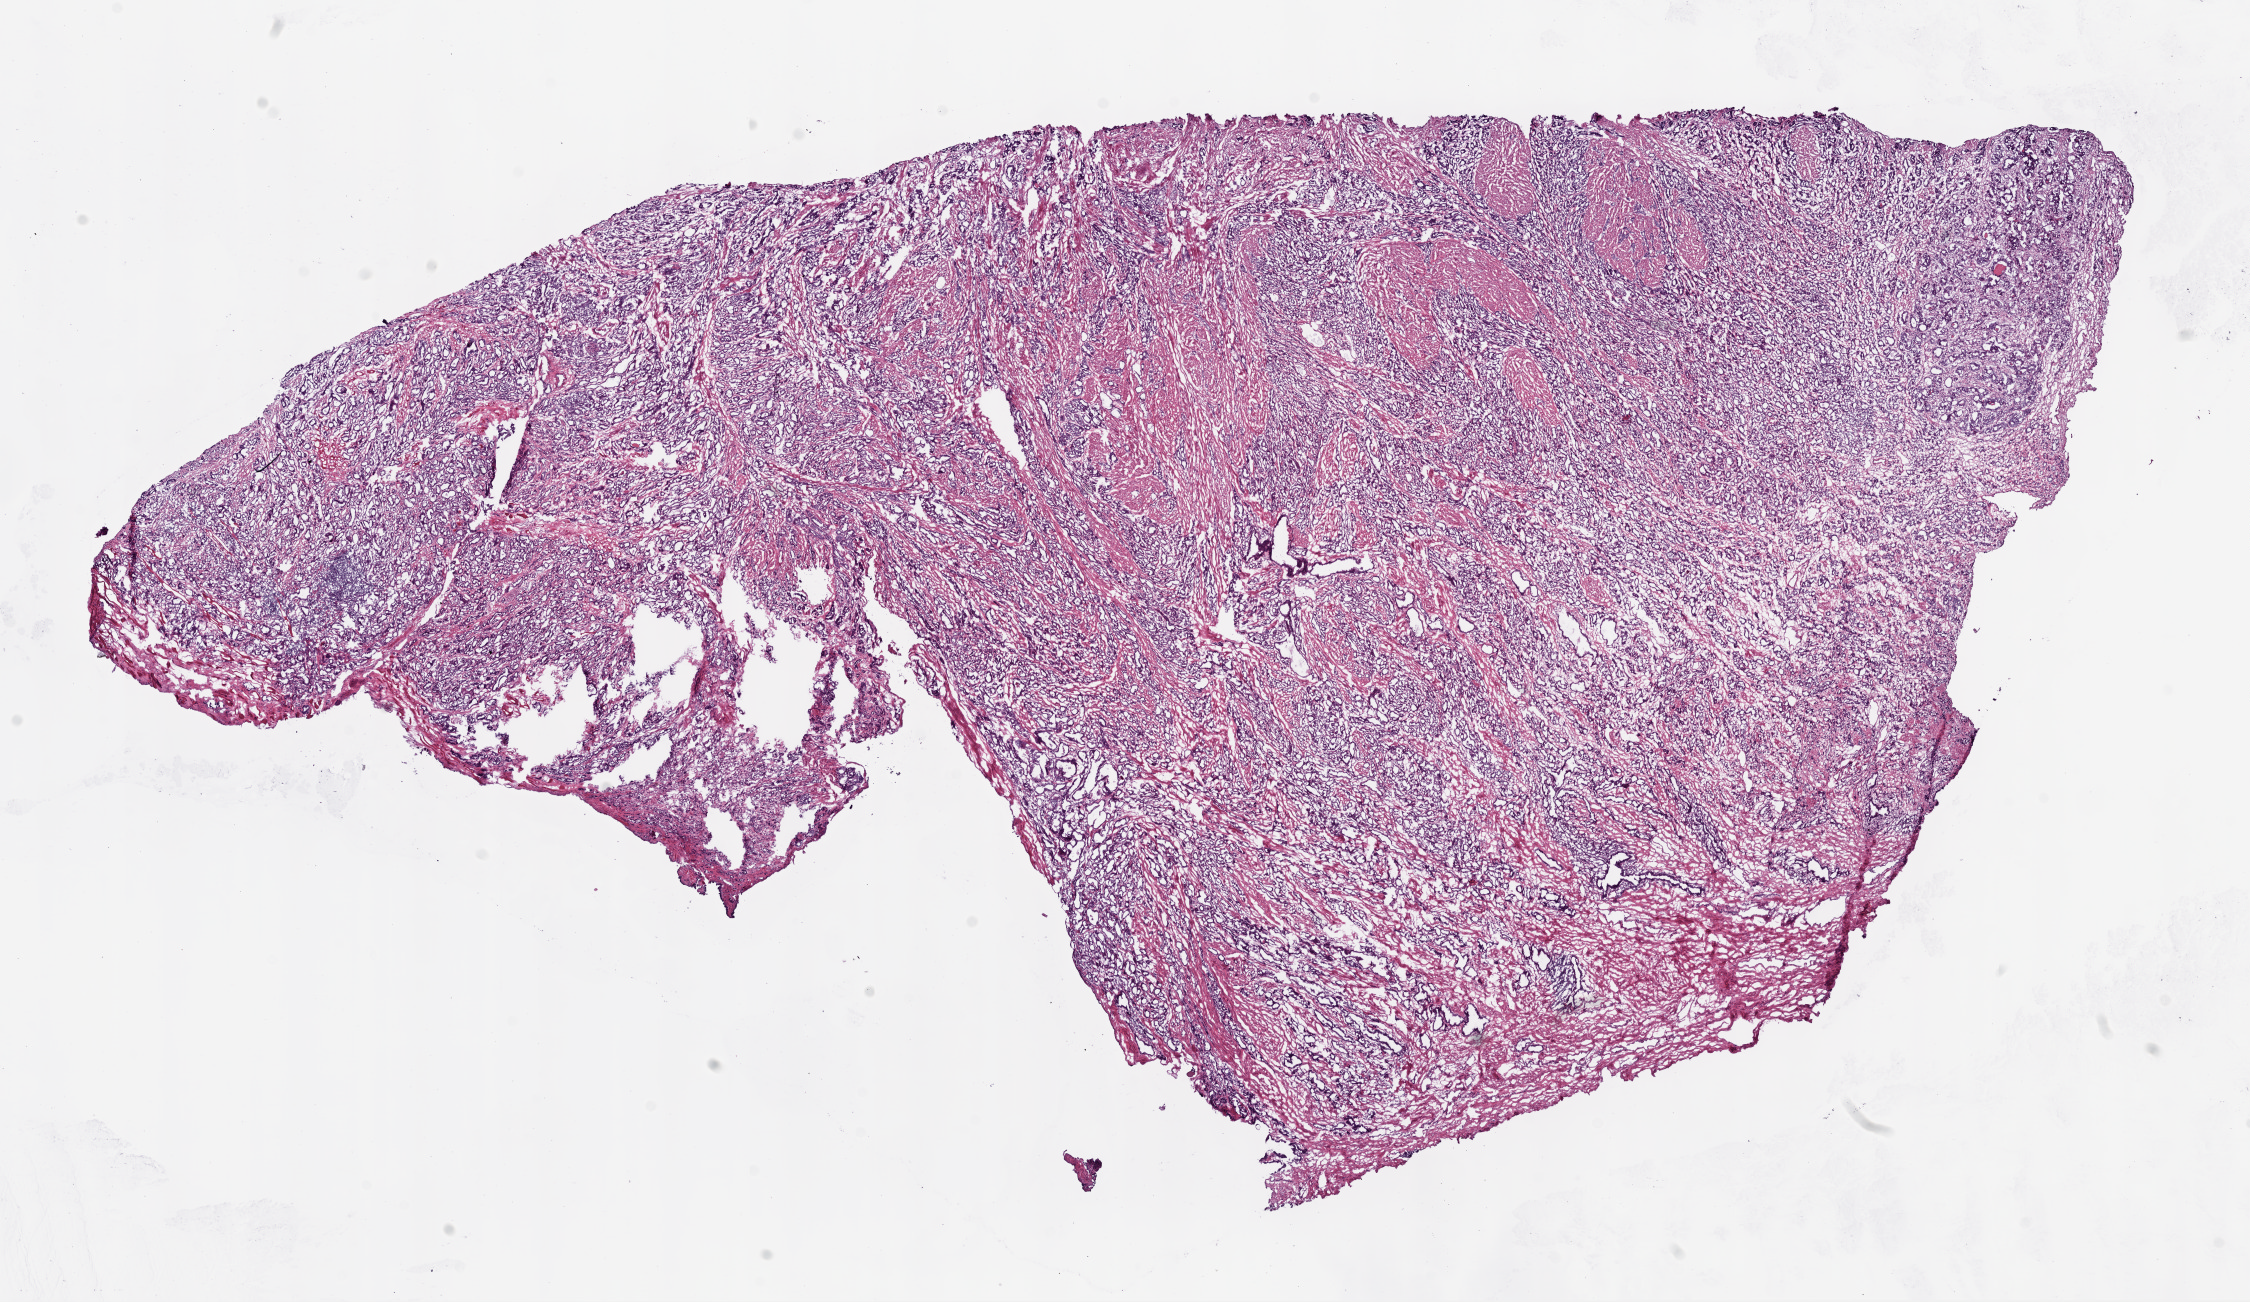
H&E whole-slide image, shown as a low-resolution overview of the whole scanned area (about 18.1 x 10.4 mm, from a 20x scan), frozen section from the top of the tissue portion, primary tumour sample from the prostate. Patient: male, age at initial diagnosis 50 years. Gleason score: 7 (4+3). Composition of this section per pathologist review: tumour cells 80%, tumour nuclei 85%, normal cells 2%, stromal cells 18%, necrosis 0%. Infiltration values recorded for this section: lymphocyte infiltration 0%, monocyte infiltration 0%, neutrophil infiltration 0%.
Laterality: bilateral. Lymph nodes positive (case pathology): 0 of 17 examined. Diagnosis: Acinar cell carcinoma (prostate gland).